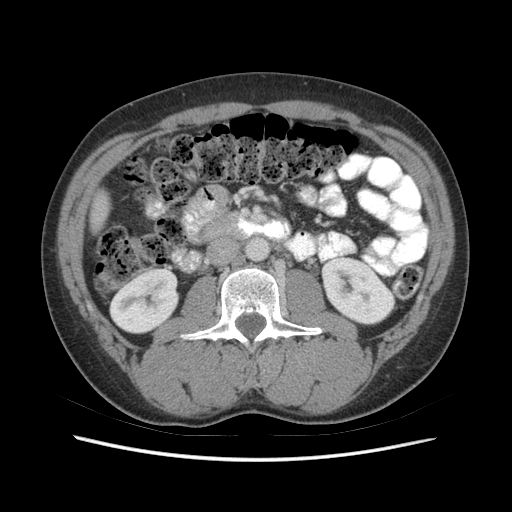
Contrast-enhanced abdominal CT (liver protocol), one axial slice; slice 9 of 73 in the series (ordered by position); soft-tissue window (W 400 / L 40 HU); 2.5 mm slice thickness; 512 × 512 image matrix, field of view 360 × 360 mm. From the clinical record (not read from this slice): diagnosis: hepatocellular carcinoma (patient treated with transarterial chemoembolisation; whether this scan precedes or follows treatment is not stated here); TNM stage (as recorded): Stage-IIIA; Child-Pugh class: A; tumour size: 6.6 cm.
Structures marked on this image (semi-automatic segmentation, software-assisted and operator-edited):
- liver parenchyma outside the tumour (the mass and vessels are separate outlines, so this box may not span the whole liver): bounding box [x1, y1, x2, y2] px = [90, 192, 108, 231]